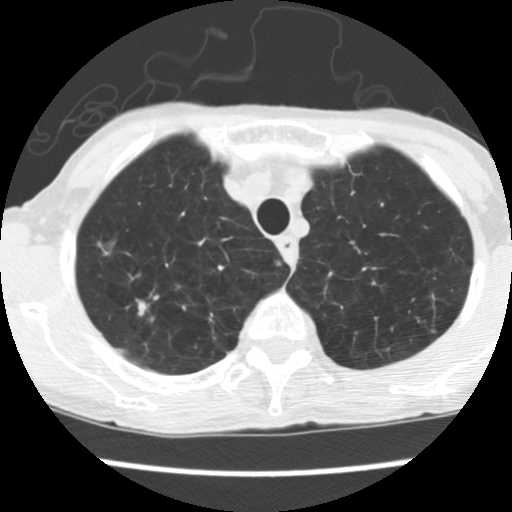
Chest CT (low-dose screening protocol), one axial image, baseline annual screen, lung window (W 1500 / L -600 HU), 2.5 mm slice thickness, standard (soft-tissue) reconstruction kernel (STANDARD), 120 kVp, slice 26 of 160 in the series, 512 × 512 image matrix. Female participant, aged 70 years at enrolment.
- Expert-annotated lung lesion, bounding box <76,224,131,271> (left, top, right, bottom; pixels).
- Screening reader's record for this exam: no non-calcified nodule ≥4 mm recorded.
- Official screen result: negative screen, significant abnormalities not suspicious for lung cancer.
- Later outcome: lung cancer diagnosed 226 days after this screen — large cell neuroendocrine carcinoma, right upper lobe, stage IA (AJCC 6th edition), 30 mm at pathology.